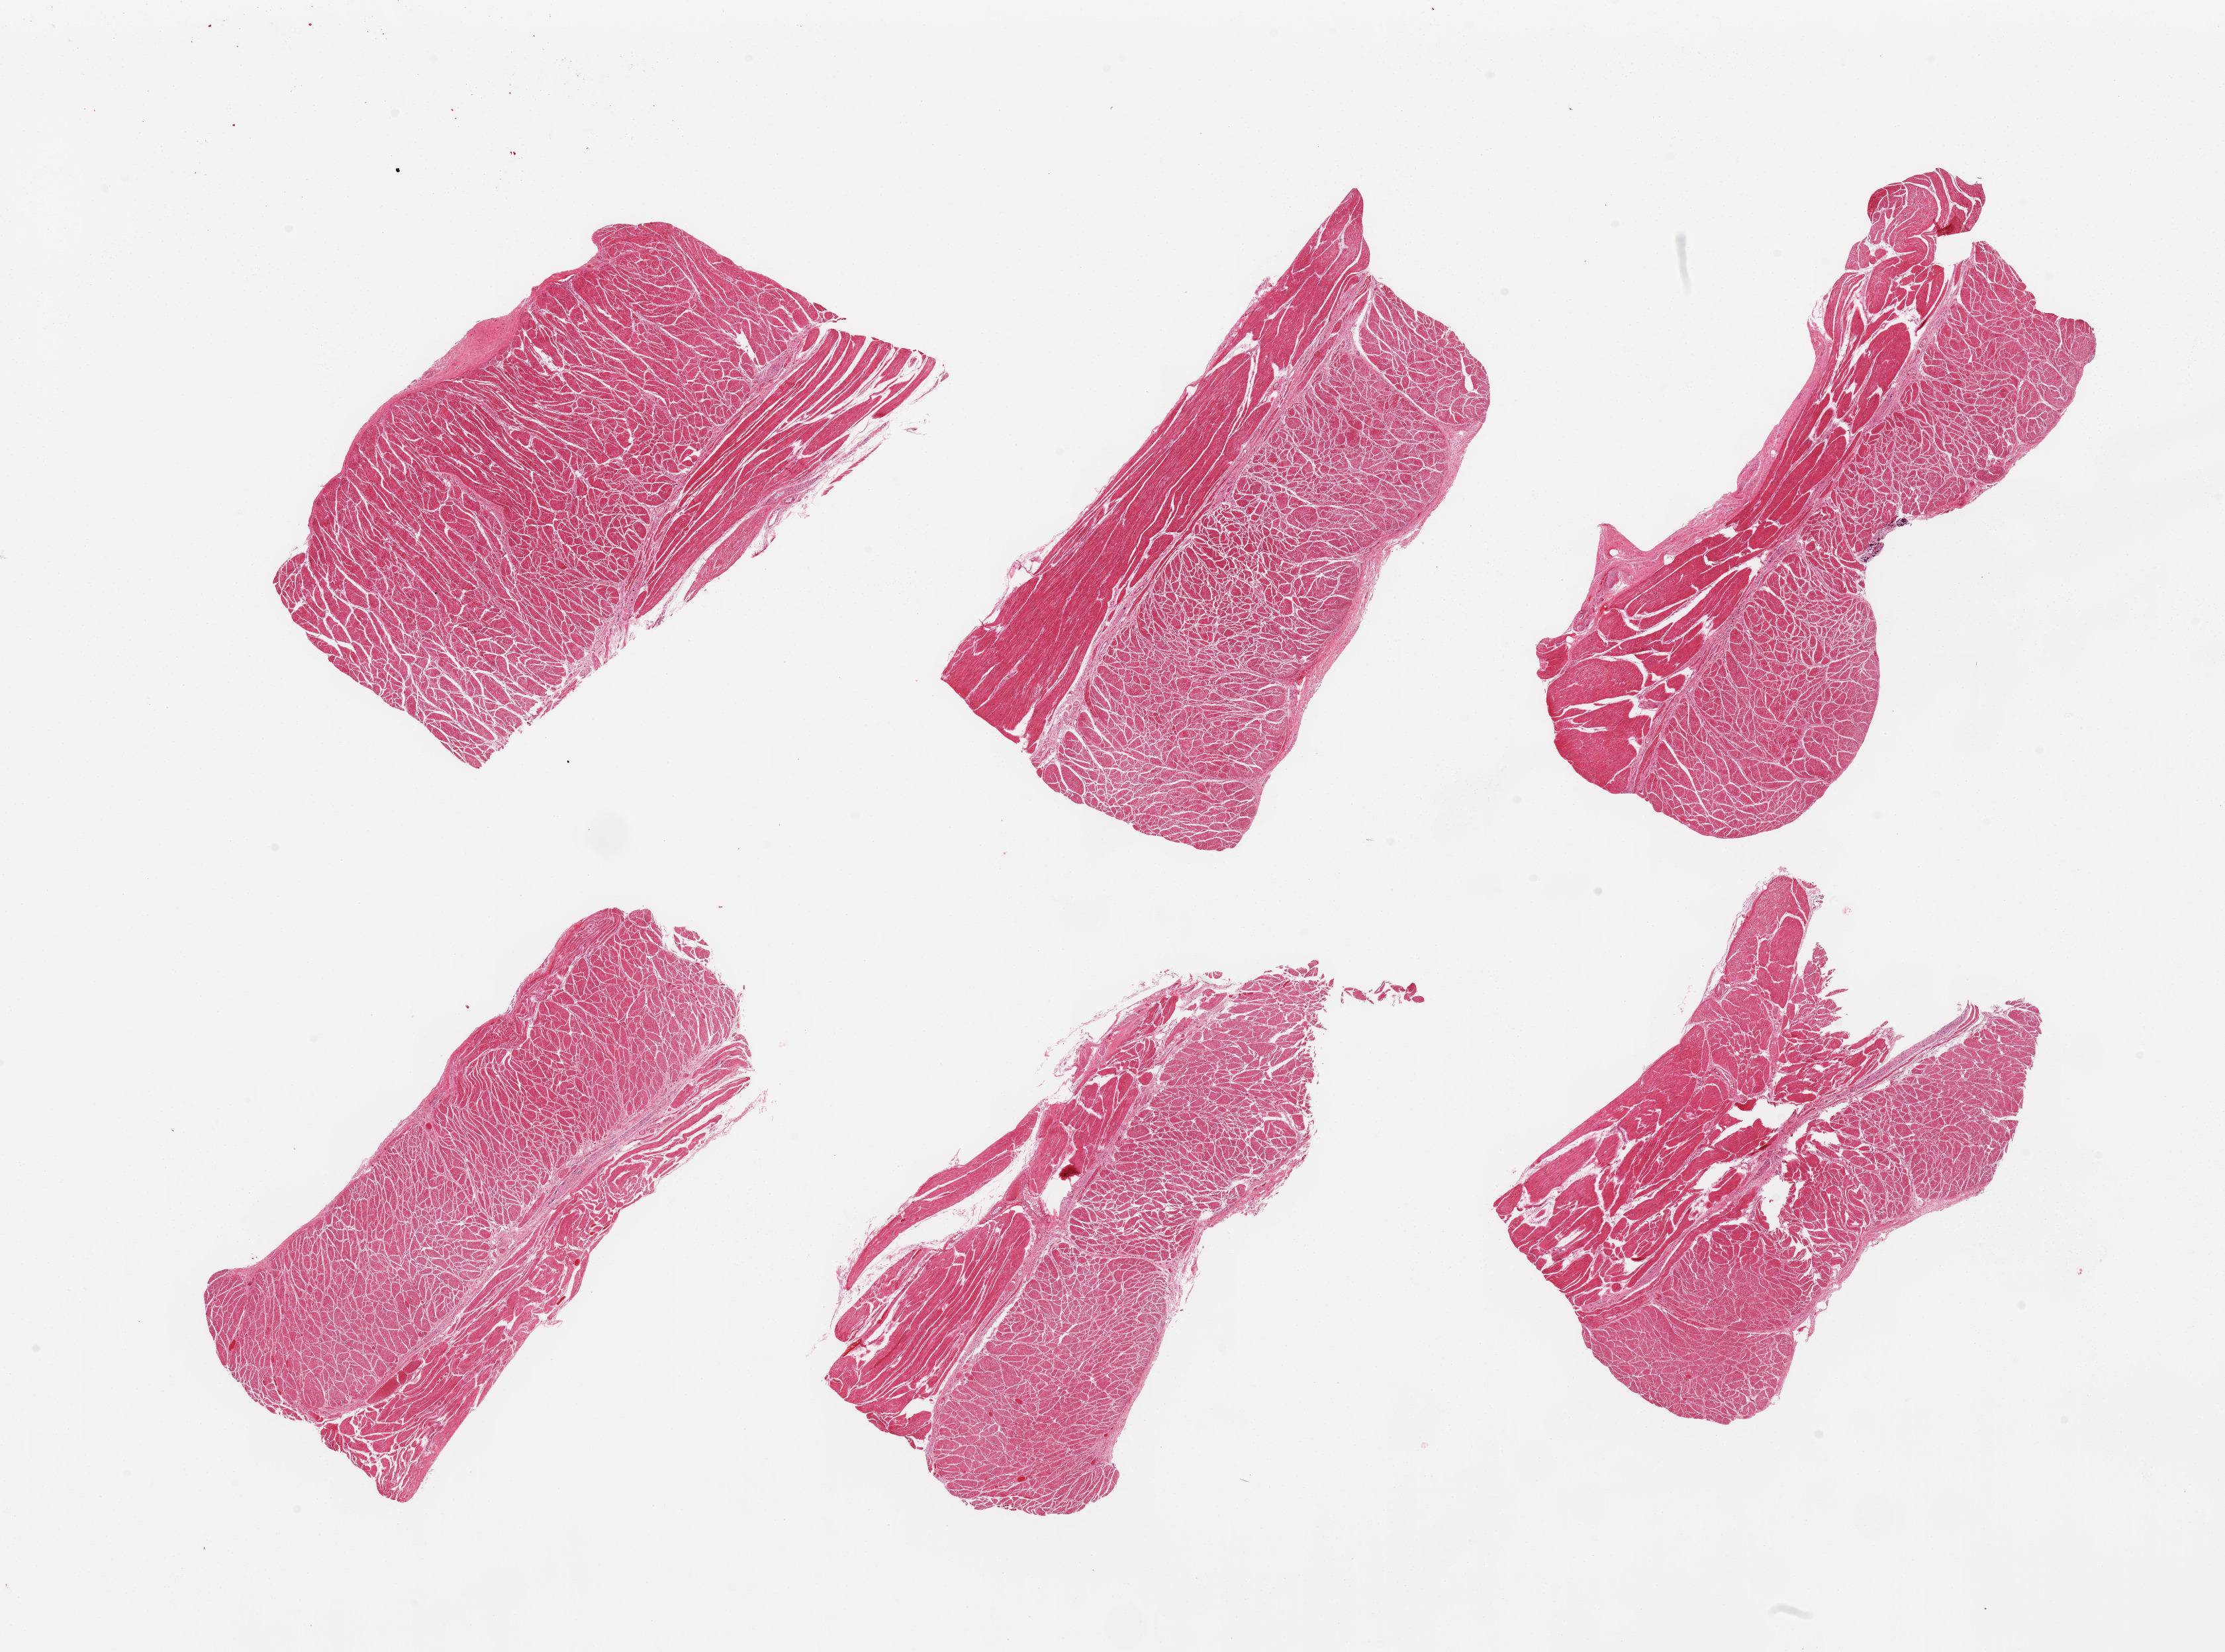
Whole-slide image, haematoxylin and eosin stain — low-resolution overview of the scanned area, about 26.6 x 19.7 mm; PAXgene-fixed, paraffin-embedded tissue; section of esophageal muscle (target tissue); tissue donor sample. Donor sex: male.
Review note (as recorded): 6 pieces; well trimmed target muscularis.